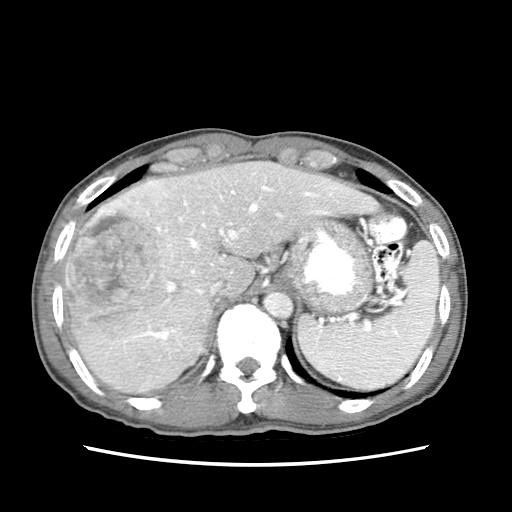
Contrast-enhanced abdominal CT (liver protocol), one axial slice; position 53 of 79 along the scan axis; 120 kVp; soft-tissue window (W 400 / L 40 HU); 2.5 mm slice thickness; 512 × 512 image matrix, field of view 320 × 320 mm. Case-level facts recorded for this patient, not image findings: diagnosis: hepatocellular carcinoma (patient treated with transarterial chemoembolisation; whether this scan precedes or follows treatment is not stated here); TNM stage (as recorded): Stage-IIIB; Child-Pugh class: A; tumour differentiation: moderately differentiated.
Outlined on this slice (semi-automatically segmented with operator editing):
- liver parenchyma outside the tumour (the mass and vessels are separate outlines, so this box may not span the whole liver): bounding box <62,160,378,394> (left, top, right, bottom; pixels)
- mass: <64,189,183,336>
- liver vessels: <103,176,344,350>